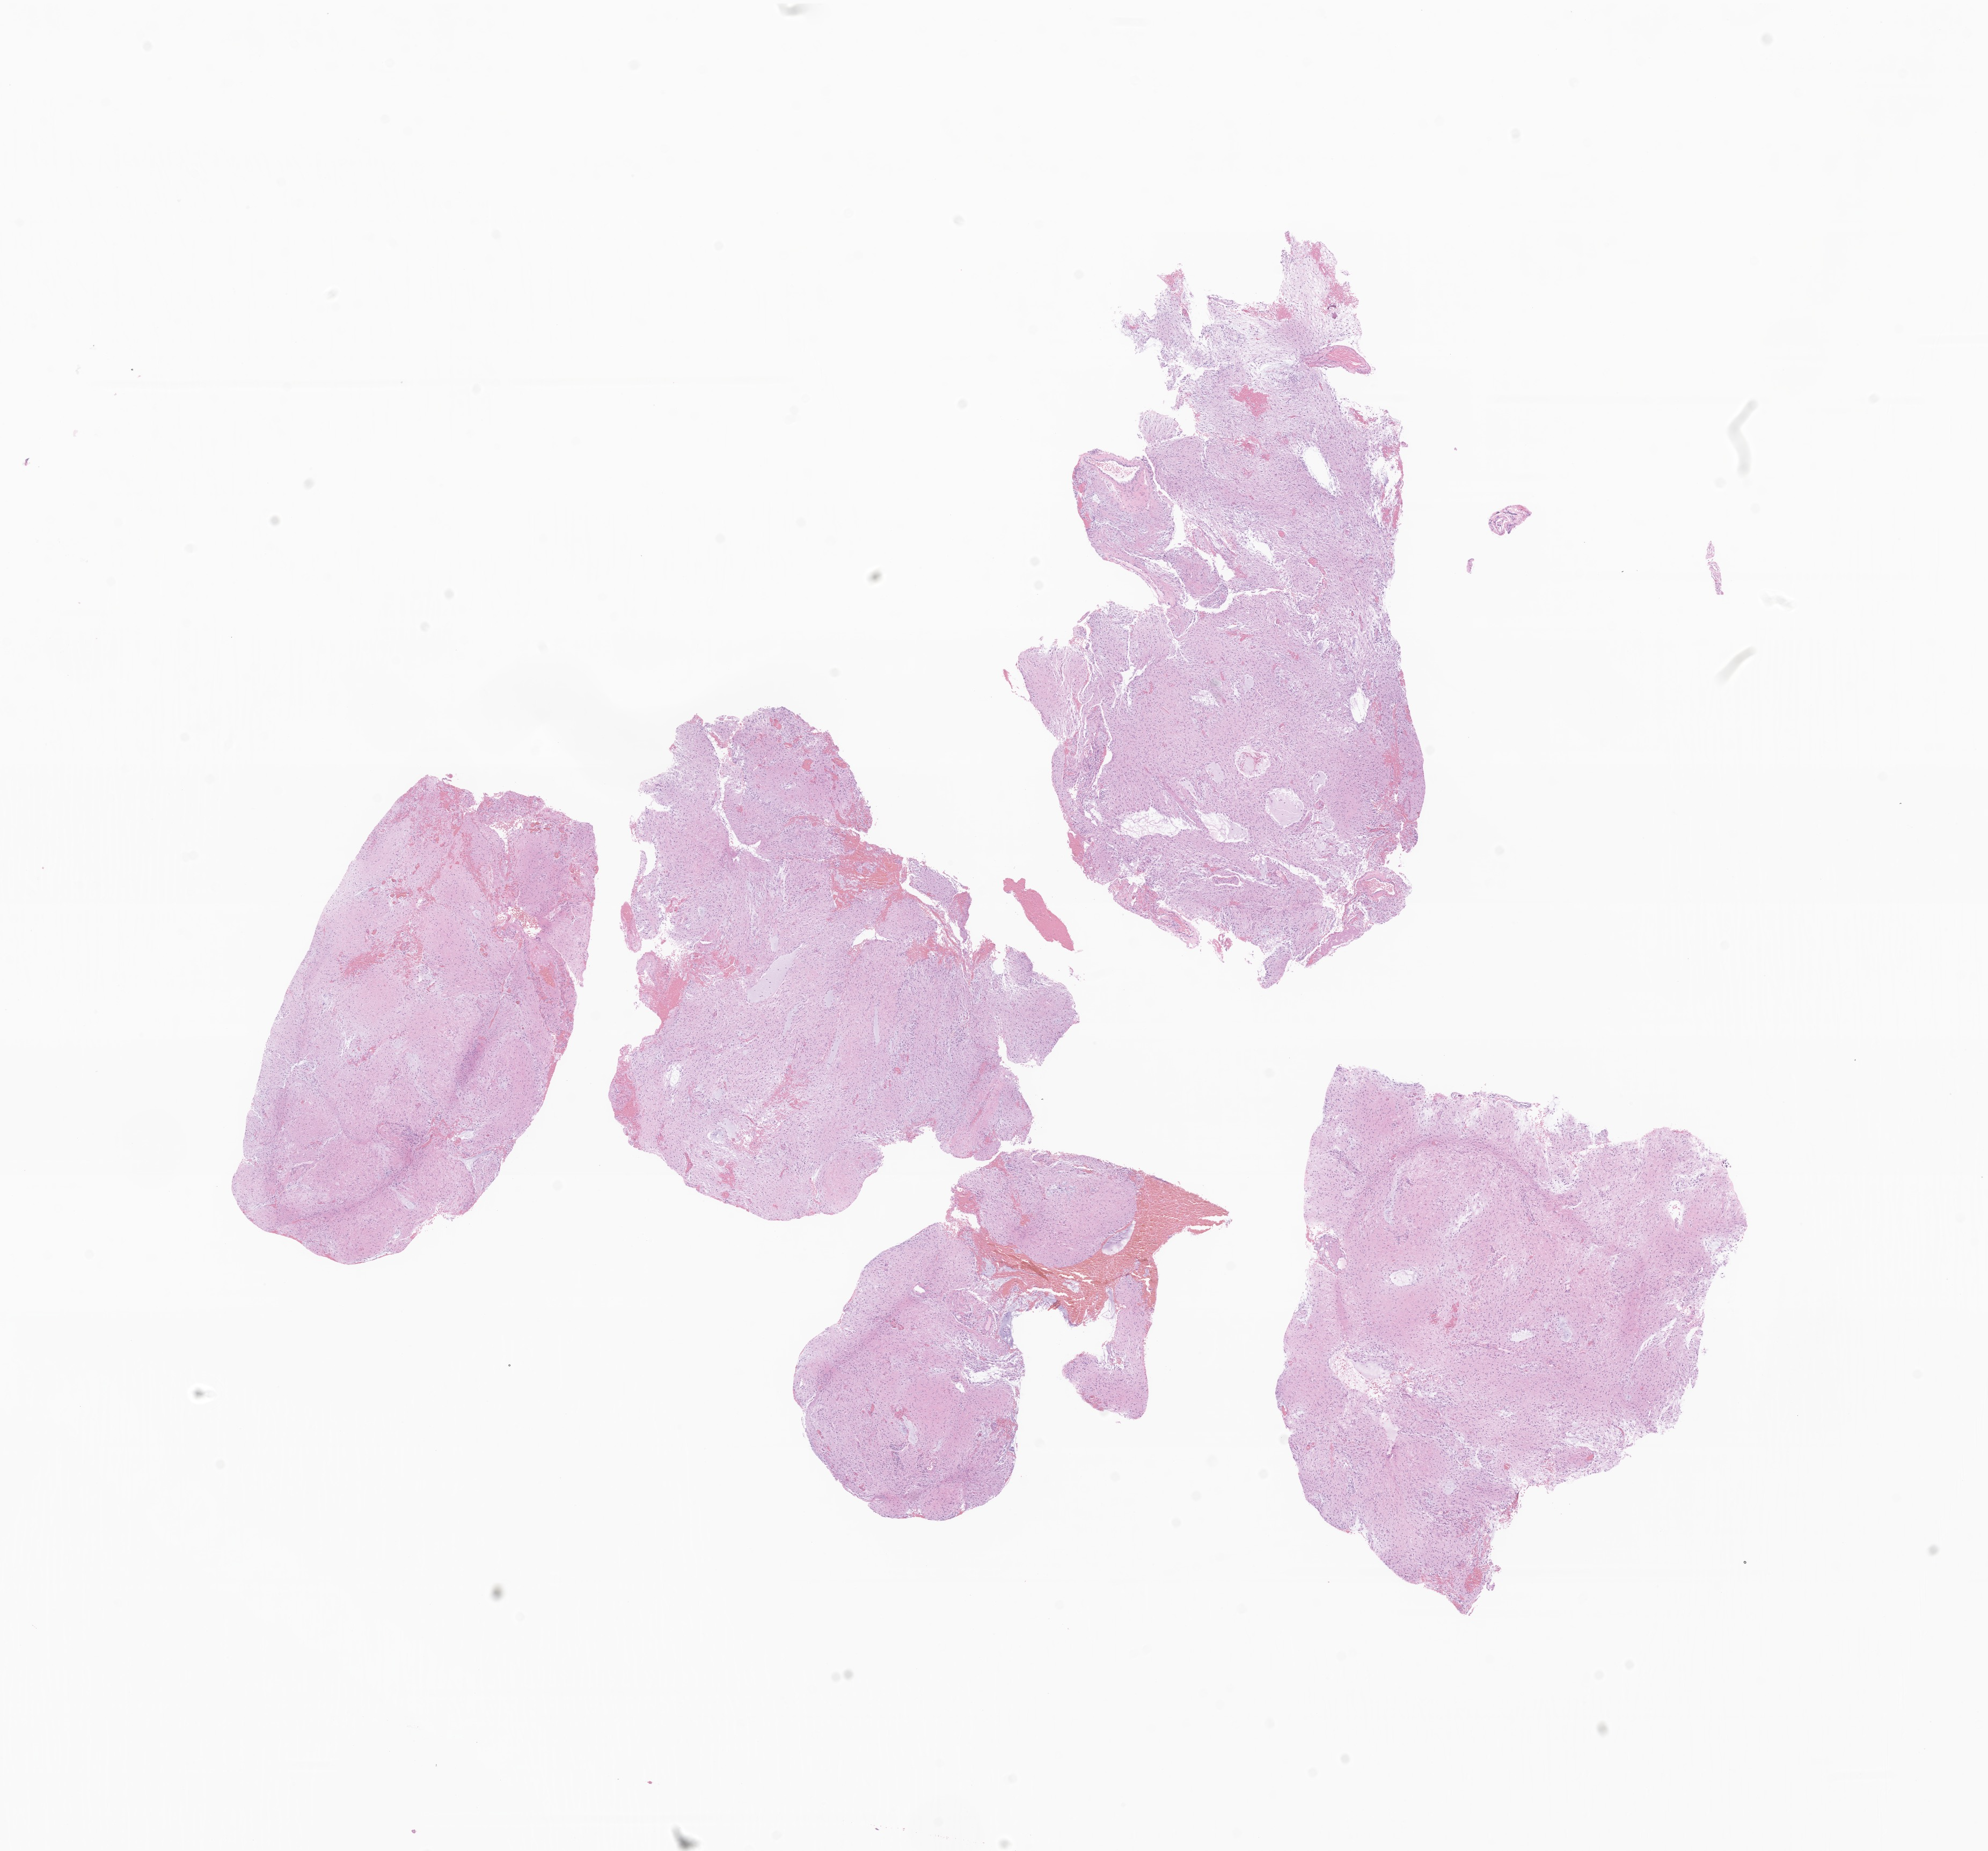
Whole-slide image, haematoxylin and eosin stain of tumor tissue from the brain, low-resolution overview of the scanned area, about 15.6 x 14.5 mm. FFPE section. Patient female; age 189 months (15 years 9 months).
Recorded diagnosis: Pilocytic astrocytoma.